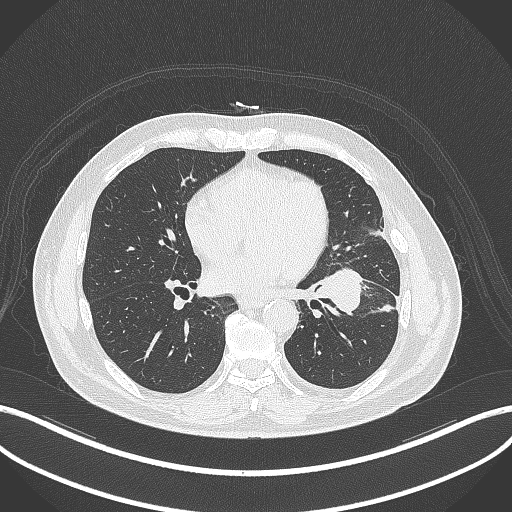
Chest CT, one axial slice. Position 157 of 230 along the scan axis. Reconstruction kernel B70f. 120 kVp. Lung window (W 1500 / L -600 HU). 1 mm slice thickness. 512 × 512 image matrix, field of view 400 × 400 mm. Patient: male, 68 years. Case-level facts recorded for this patient, not image findings: clinical TNM (as recorded): T2b N0 M0.
Structures marked on this image (bounding box drawn by a radiologist):
- lung tumour (recorded histology: squamous cell carcinoma): bounding box <314,264,364,318> (left, top, right, bottom; pixels)